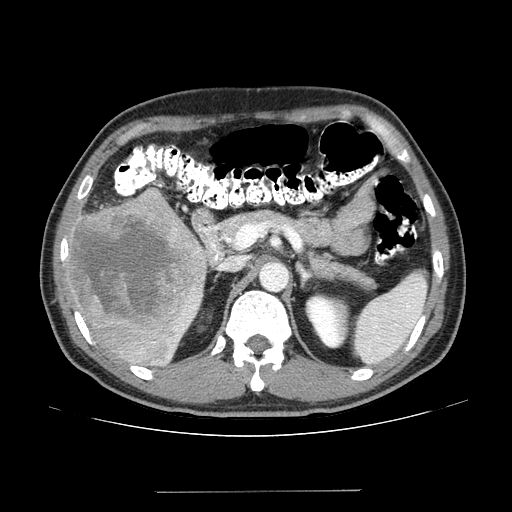
Contrast-enhanced abdominal CT (liver protocol), one axial slice. Position 76 of 131 along the scan axis. 100 kVp. One of 2 acquisitions stored at this slice position. Soft-tissue window (W 400 / L 40 HU). 2.5 mm slice thickness. 512 × 512 image matrix, field of view 380 × 380 mm. Case-level facts recorded for this patient, not image findings: diagnosis: hepatocellular carcinoma (patient treated with transarterial chemoembolisation; whether this scan precedes or follows treatment is not stated here); TNM stage (as recorded): Stage-I; Child-Pugh class: A; tumour nodularity: uninodular; tumour size: 10.3 cm.
Outlined on this slice (semi-automatic segmentation, software-assisted and operator-edited):
- liver parenchyma outside the tumour (the mass and vessels are separate outlines, so this box may not span the whole liver): bounding box [x1, y1, x2, y2] px = [64, 188, 206, 366]
- mass: [71, 191, 204, 332]
- liver vessels: [176, 307, 195, 330]